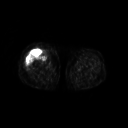
FDG PET of an extremity soft-tissue mass (from a PET/CT study), one axial slice. 128 × 128 image matrix. Female patient, age 57 years. Case-level facts recorded for this patient, not image findings: histological type: pleiomorphic undifferentiated sarcoma; grade: high; site of the primary tumour: right quadricep.
Structures marked on this image (expert contour drawn on MRI and transferred to this co-registered scan by the dataset authors):
- tumour plus oedema (research contour): bounding box (x1, y1, x2, y2) in pixels: (25, 50, 45, 70)